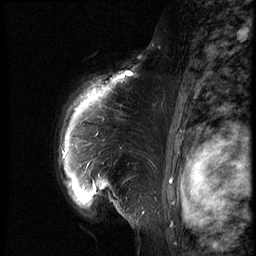
Breast MRI (dynamic contrast-enhanced), one sagittal slice; slice 52 of 66 in the series (ordered by position); dynamic contrast-enhanced series, image 2 of 3 at this slice position (ordered by acquisition); 1.5 T; TE 4.2 ms, TR 8.9 ms; 256 × 256 image matrix, field of view 200 × 200 mm. Female patient, age 39 years. From the clinical record (not read from this slice): setting: breast cancer imaged before/during neoadjuvant chemotherapy; receptor status: HER2-positive.
Annotated regions visible in this slice (semi-automatically segmented with operator editing):
- analysis volume of interest (the breast-tissue region the enhancement analysis was run in; not a lesion): bounding box (x1, y1, x2, y2) in pixels: (52, 75, 167, 218)
- tumour enhancement mask (voxels above the 140 % enhancement threshold inside the analysis volume of interest): (129, 75, 133, 77)